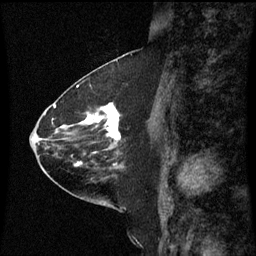
Breast MRI (dynamic contrast-enhanced), one sagittal slice. Position 29 of 60 along the scan axis. Dynamic contrast-enhanced series, image 2 of 3 at this slice position (ordered by acquisition). 1.5 T. TE 4.2 ms, TR 8.9 ms. 2 mm slice thickness. 256 × 256 image matrix, field of view 200 × 200 mm. Patient: female, 63 years. Case-level facts recorded for this patient, not image findings: setting: breast cancer imaged before/during neoadjuvant chemotherapy; receptor status: HR-positive, HER2-negative.
Annotated regions visible in this slice (semi-automatic segmentation, software-assisted and operator-edited):
- analysis volume of interest (the breast-tissue region the enhancement analysis was run in; not a lesion): bounding box [x1, y1, x2, y2] px = [77, 104, 125, 151]
- tumour enhancement mask (voxels above the 70 % enhancement threshold inside the analysis volume of interest): [81, 104, 120, 141]